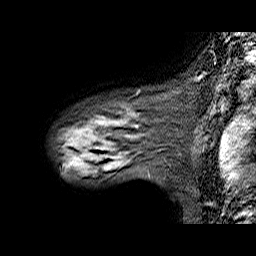
Breast MRI (dynamic contrast-enhanced), one sagittal slice. Position 49 of 60 along the scan axis. Dynamic contrast-enhanced series, time point 2 of 6 at this slice position (early post-contrast). 1.5 T. TE 6.3 ms, TR 32.9 ms. 256 × 256 image matrix, field of view 200 × 200 mm. Female patient. From the clinical record (not read from this slice): setting: breast cancer imaged before/during neoadjuvant chemotherapy; receptor status: HER2-positive.
Outlined on this slice (semi-automatically segmented with operator editing):
- analysis volume of interest (the breast-tissue region the enhancement analysis was run in; not a lesion): bounding box [x1, y1, x2, y2] px = [59, 88, 174, 173]
- tumour enhancement mask (voxels above the 100 % enhancement threshold inside the analysis volume of interest): [105, 167, 110, 170]